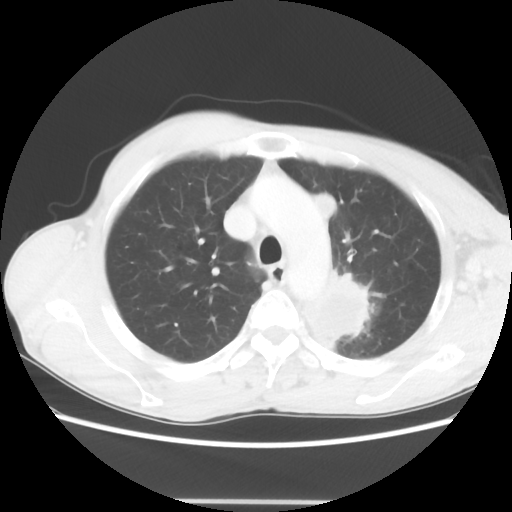
Chest CT, one axial slice. Lung window (W 1500 / L -600 HU). 5 mm slice thickness. 512 × 512 image matrix, field of view 360 × 360 mm. Patient: male, 61 years. From the clinical record (not read from this slice): clinical TNM (as recorded): T3 N1 M1.
Structures marked on this image (rectangle marked by the reading radiologist):
- lung tumour (recorded histology: adenocarcinoma): bounding box [x1, y1, x2, y2] px = [295, 271, 365, 359]
- lung tumour (recorded histology: adenocarcinoma): [303, 188, 337, 226]